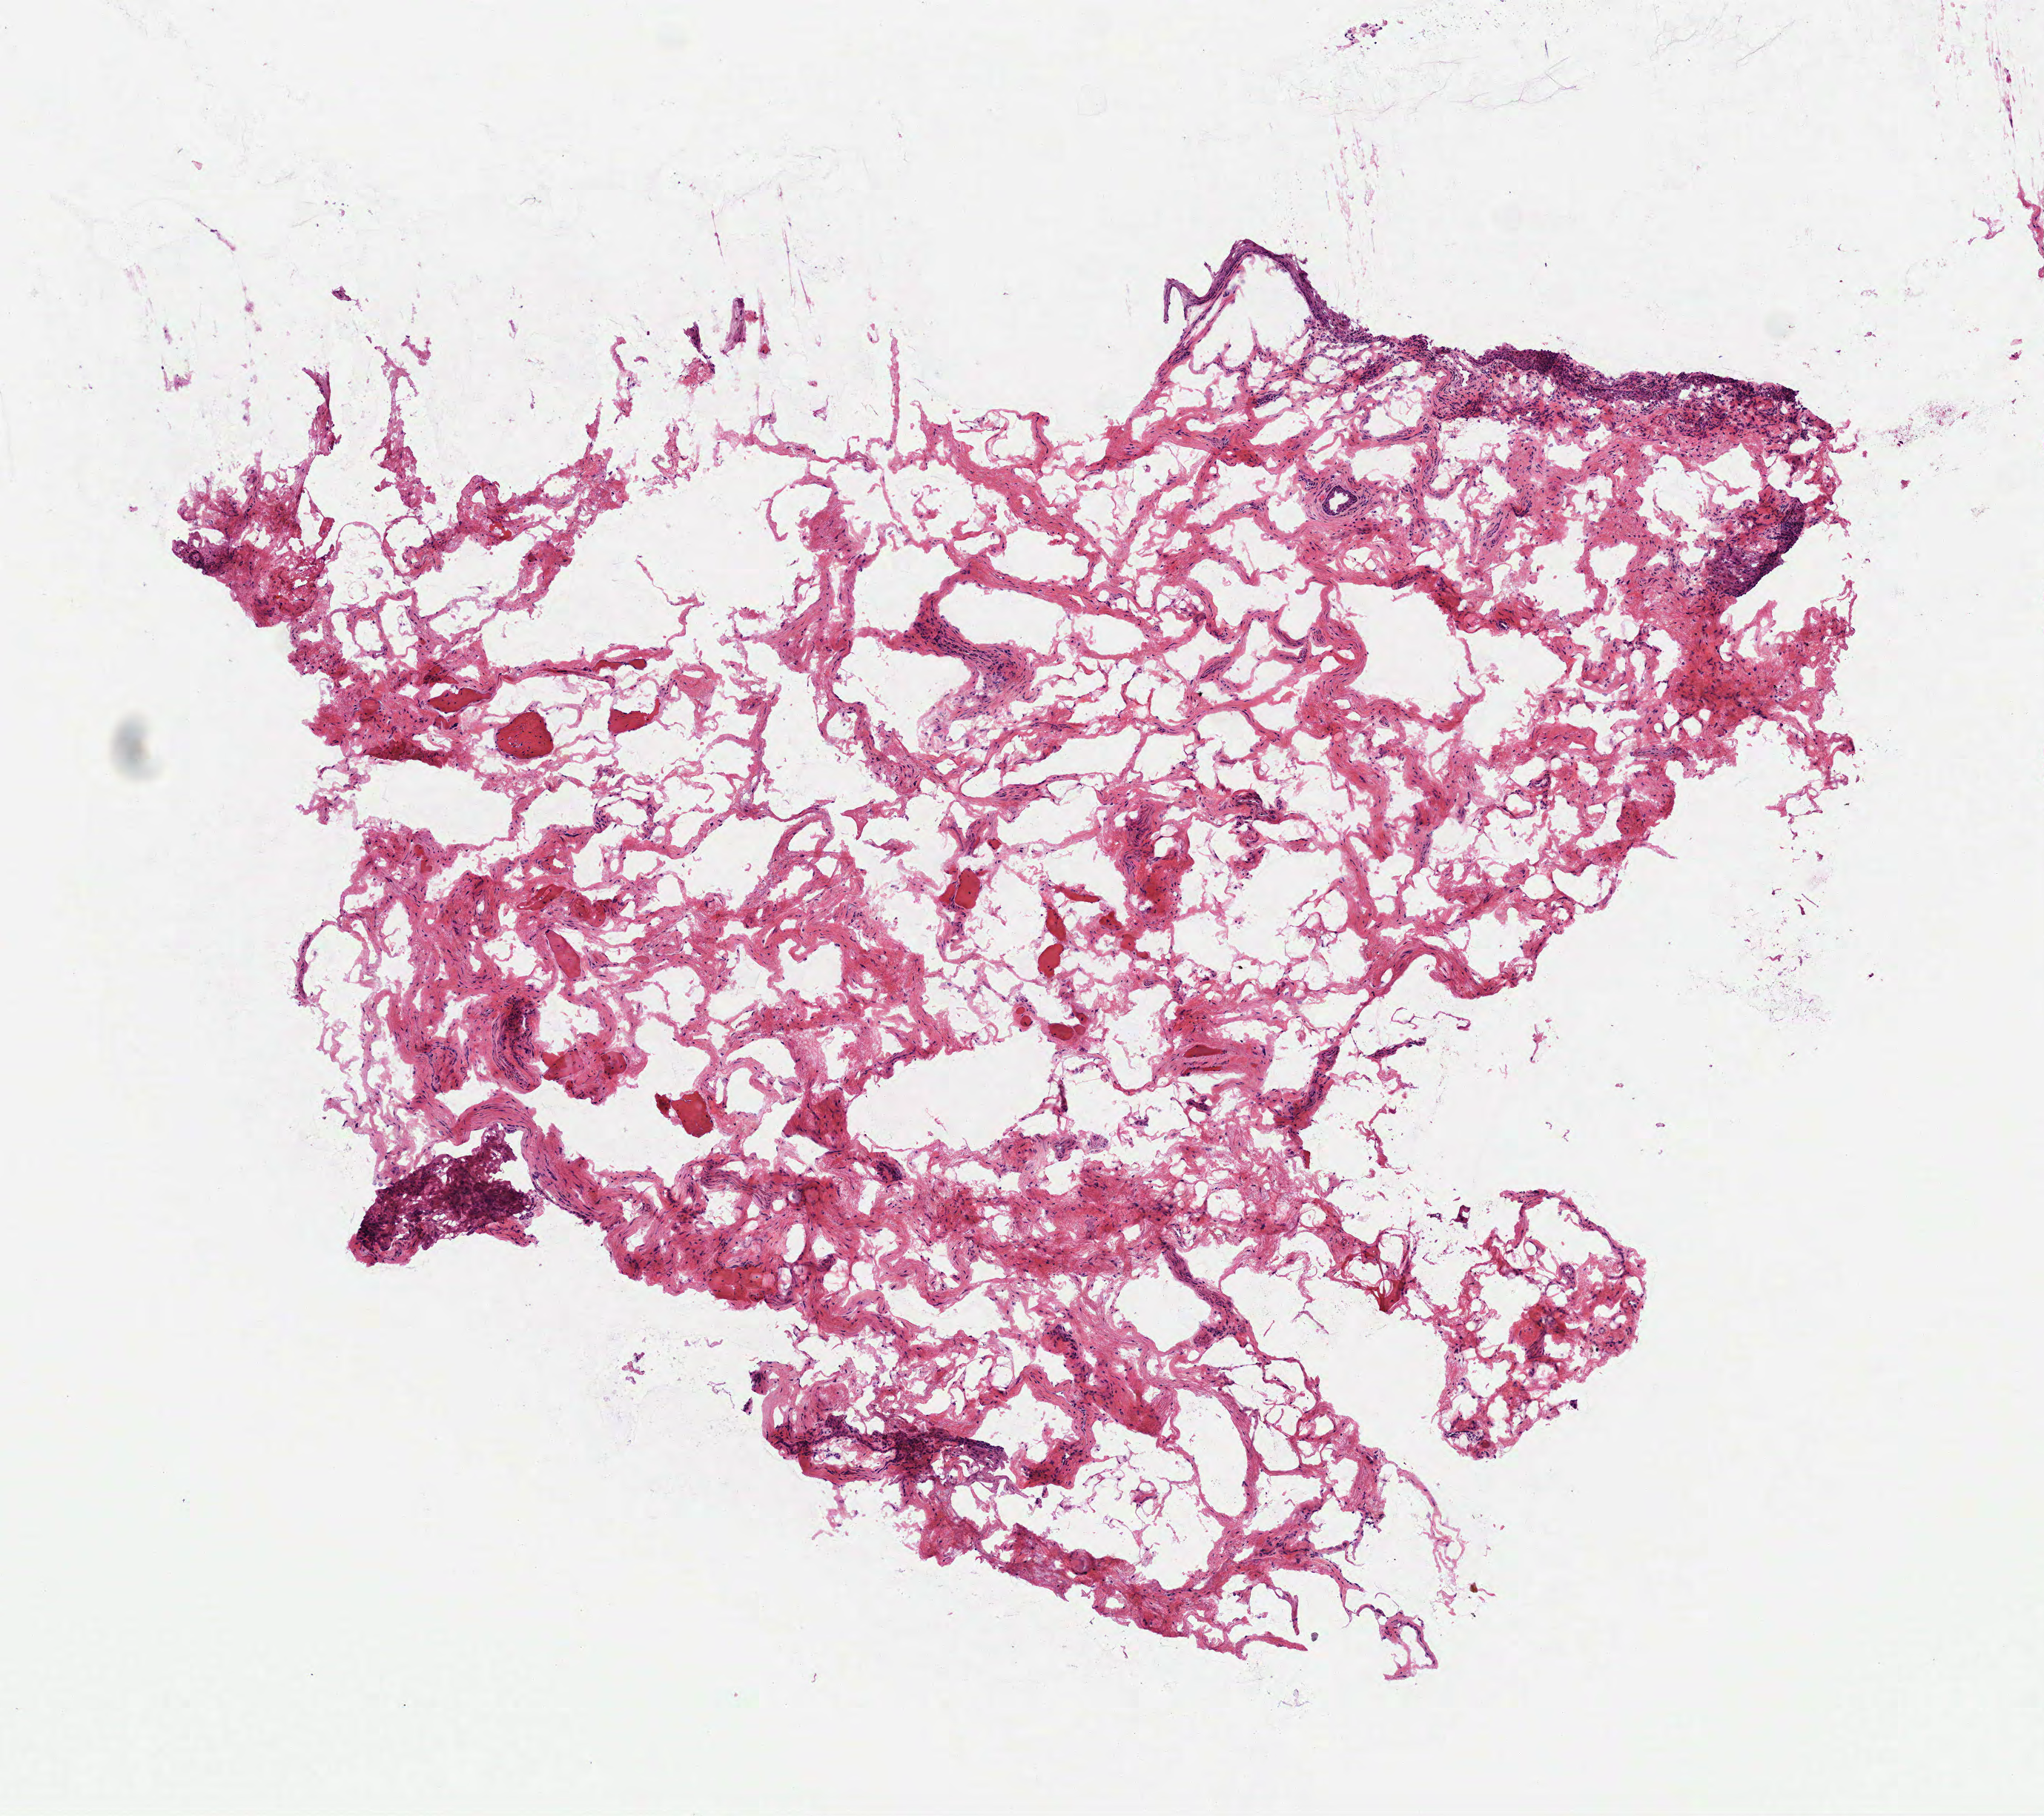
Whole-slide histology image, H&E — whole scanned area (about 5.6 x 4.9 mm, from a 40x scan) shown as a low-resolution overview. Frozen section. Sample: solid tissue normal (non-tumour tissue), head and neck. Patient: female, age at initial diagnosis 32 years.
This section: solid tissue normal (non-tumour) sample from the same patient. Patient diagnosis: Squamous cell carcinoma, NOS (tongue, NOS).